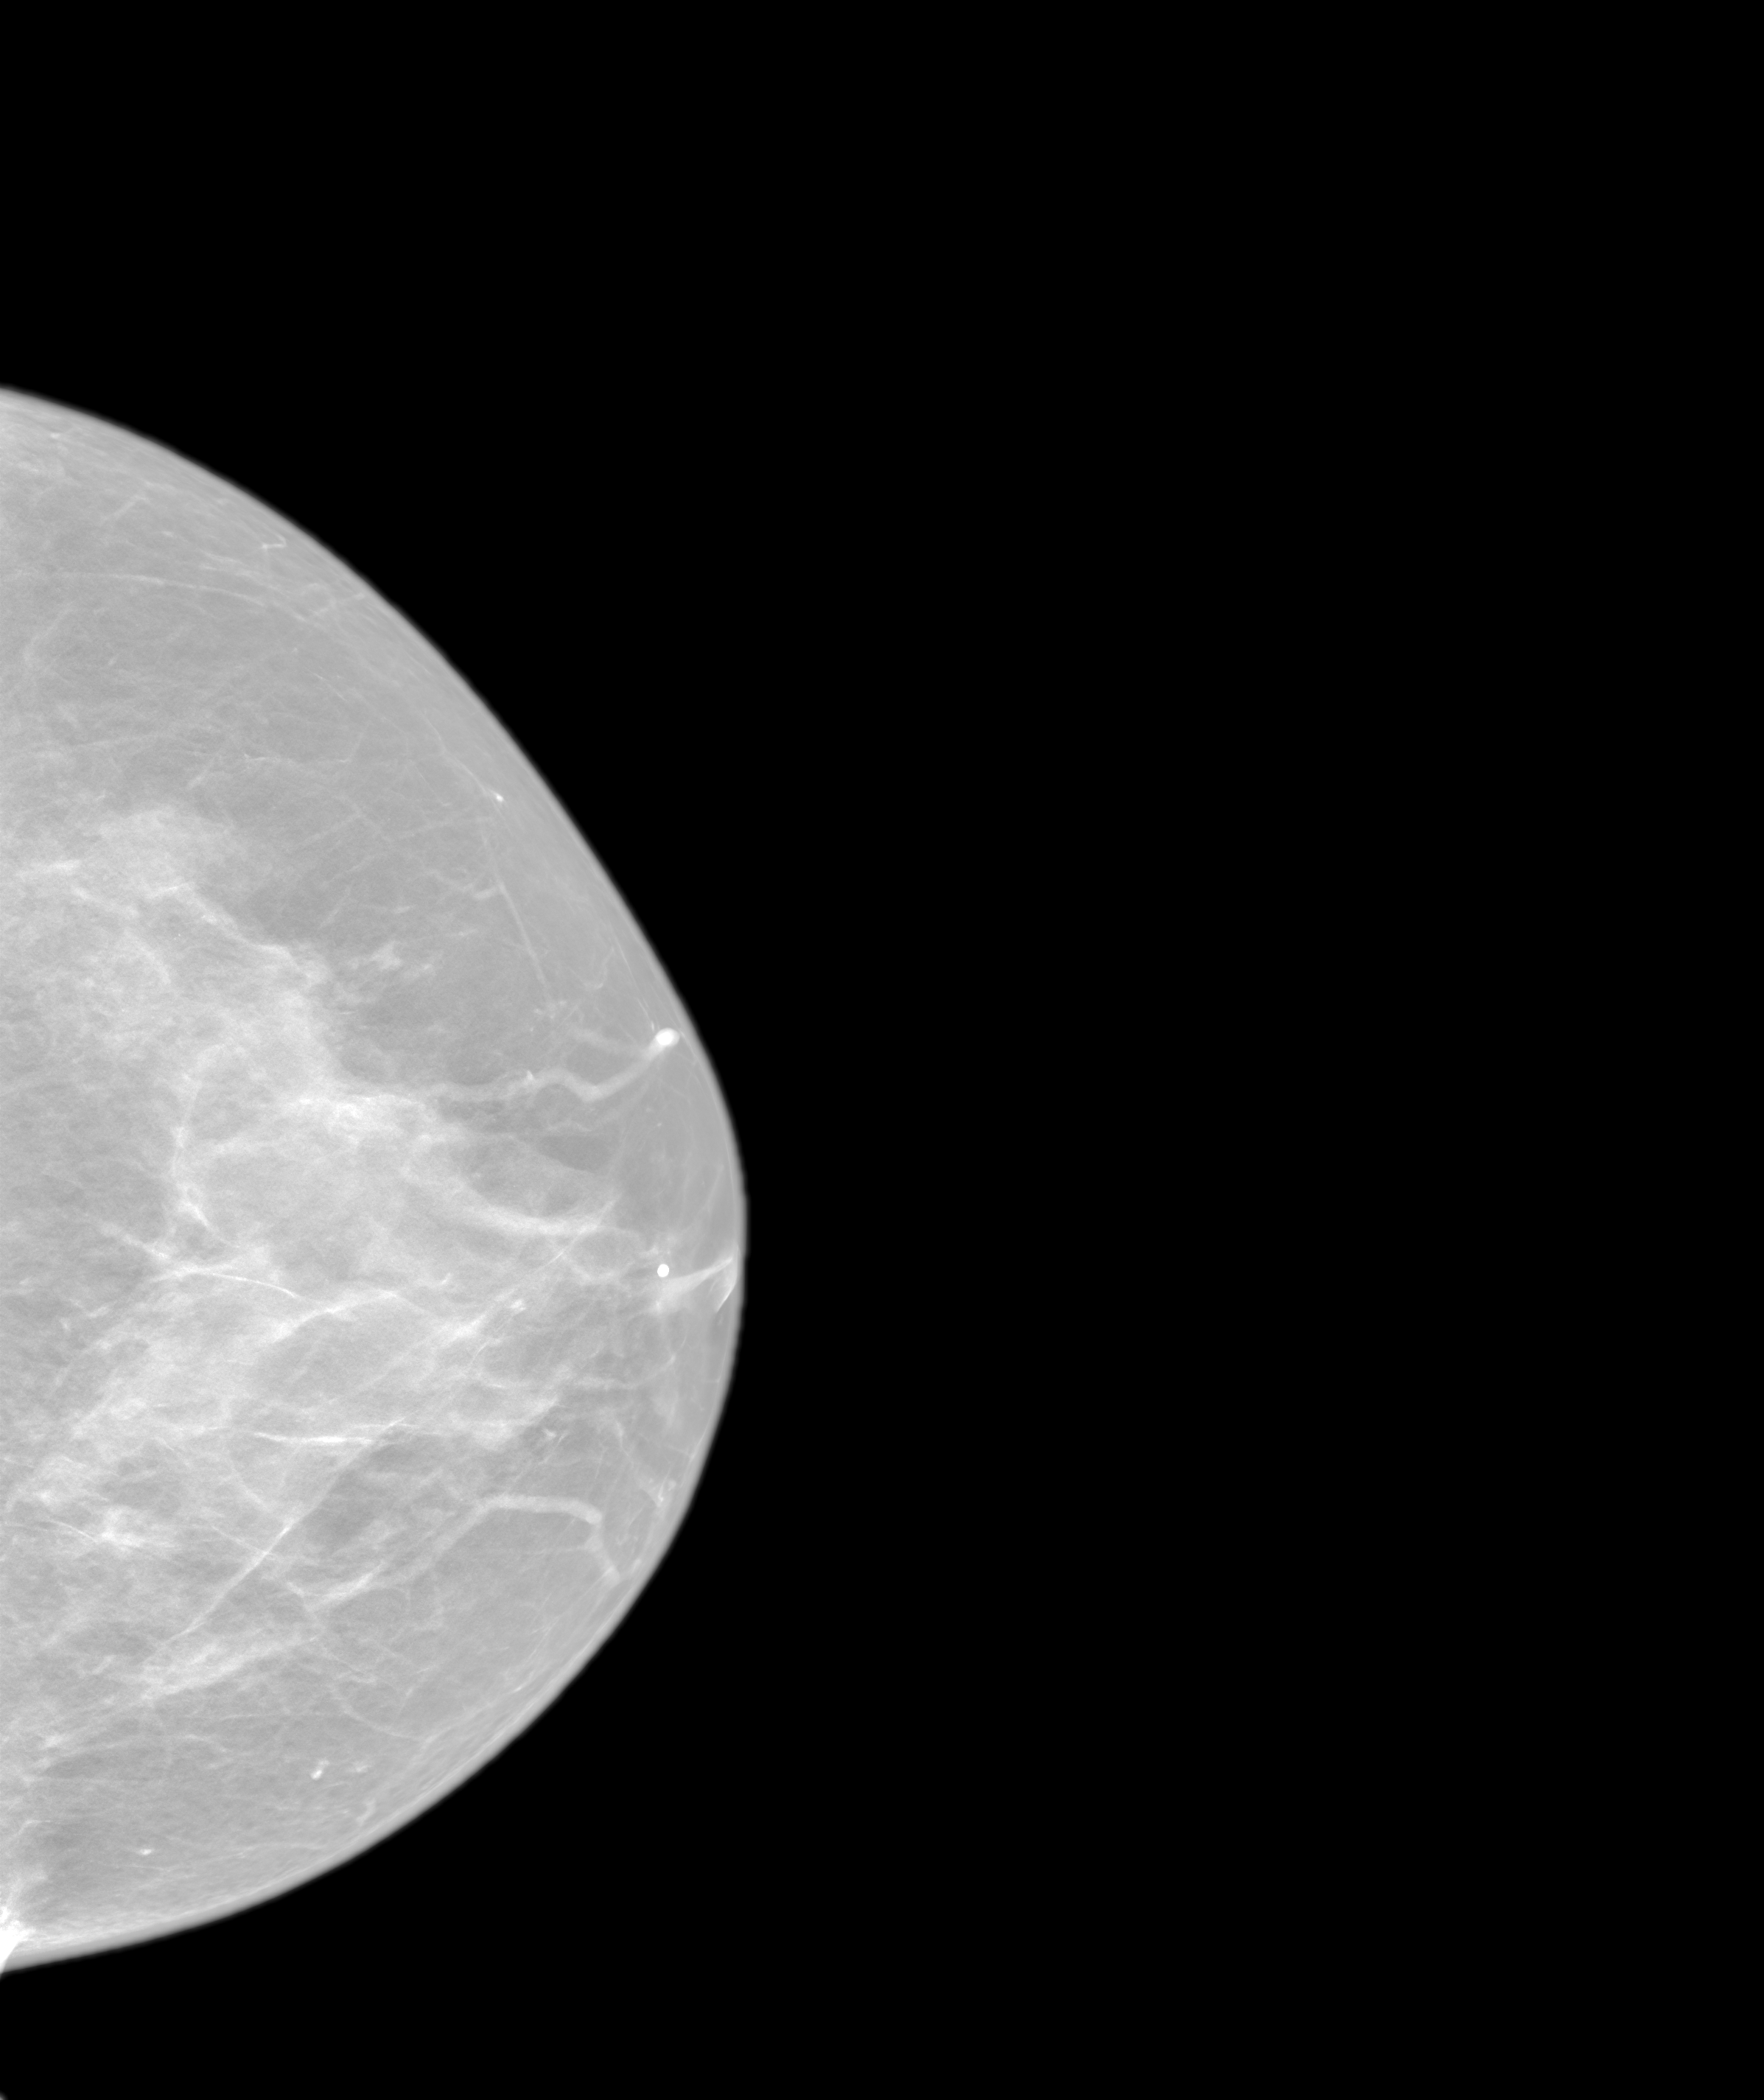
Screening examination; system: SenoIris_1SP2(440). Patient: female, 48 years.
Image type: synthesized 2-D view from tomosynthesis. Breast: left. Projection: cranio-caudal projection.